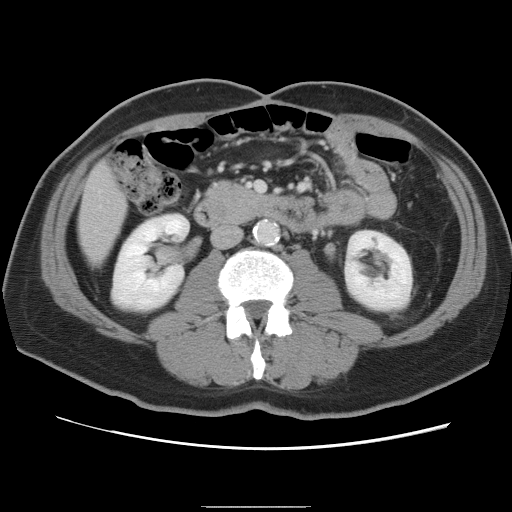
Contrast-enhanced abdominal CT, one axial slice; slice 22 of 87 in the series (ordered by position); 120 kVp; intravenous contrast given; soft-tissue window (W 400 / L 40 HU); 5 mm slice thickness; 512 × 512 image matrix, field of view 363 × 363 mm. Male patient, age 63 years. From the clinical record (not read from this slice): diagnosis: colorectal cancer liver metastases, imaged before liver resection; multiple liver metastases: no; largest metastasis: 9 cm; disease in both lobes: no.
Annotated regions visible in this slice (outlined manually by an expert reader):
- liver: box from (x=79, y=165) to (x=127, y=264) px
- planned liver remnant (the part of the liver to remain after resection): (x=80, y=165)–(x=127, y=264)